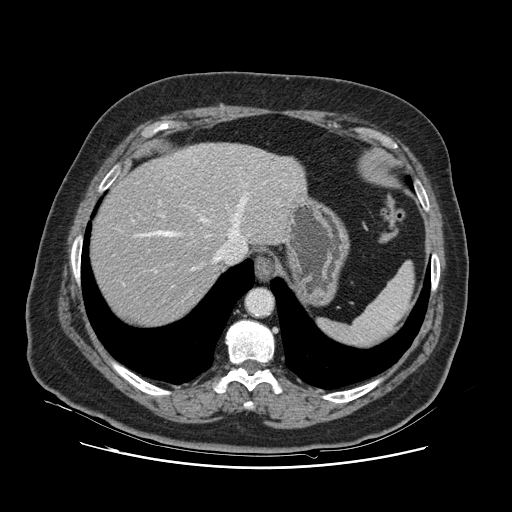
Contrast-enhanced abdominal CT, one axial slice. Position 99 of 132 along the scan axis. Soft-tissue window (W 400 / L 40 HU). 2.5 mm slice thickness. 512 × 512 image matrix, field of view 391 × 391 mm. Female patient, age 73 years. From the clinical record (not read from this slice): diagnosis: colorectal cancer liver metastases, imaged before liver resection; multiple liver metastases: no.
Structures marked on this image (expert manual segmentation):
- hepatic veins: bounding box <123,178,246,285> (left, top, right, bottom; pixels)
- liver: <91,144,304,326>
- planned liver remnant (the part of the liver to remain after resection): <92,162,229,326>
- portal vein (with intrahepatic branches): <154,200,165,272>